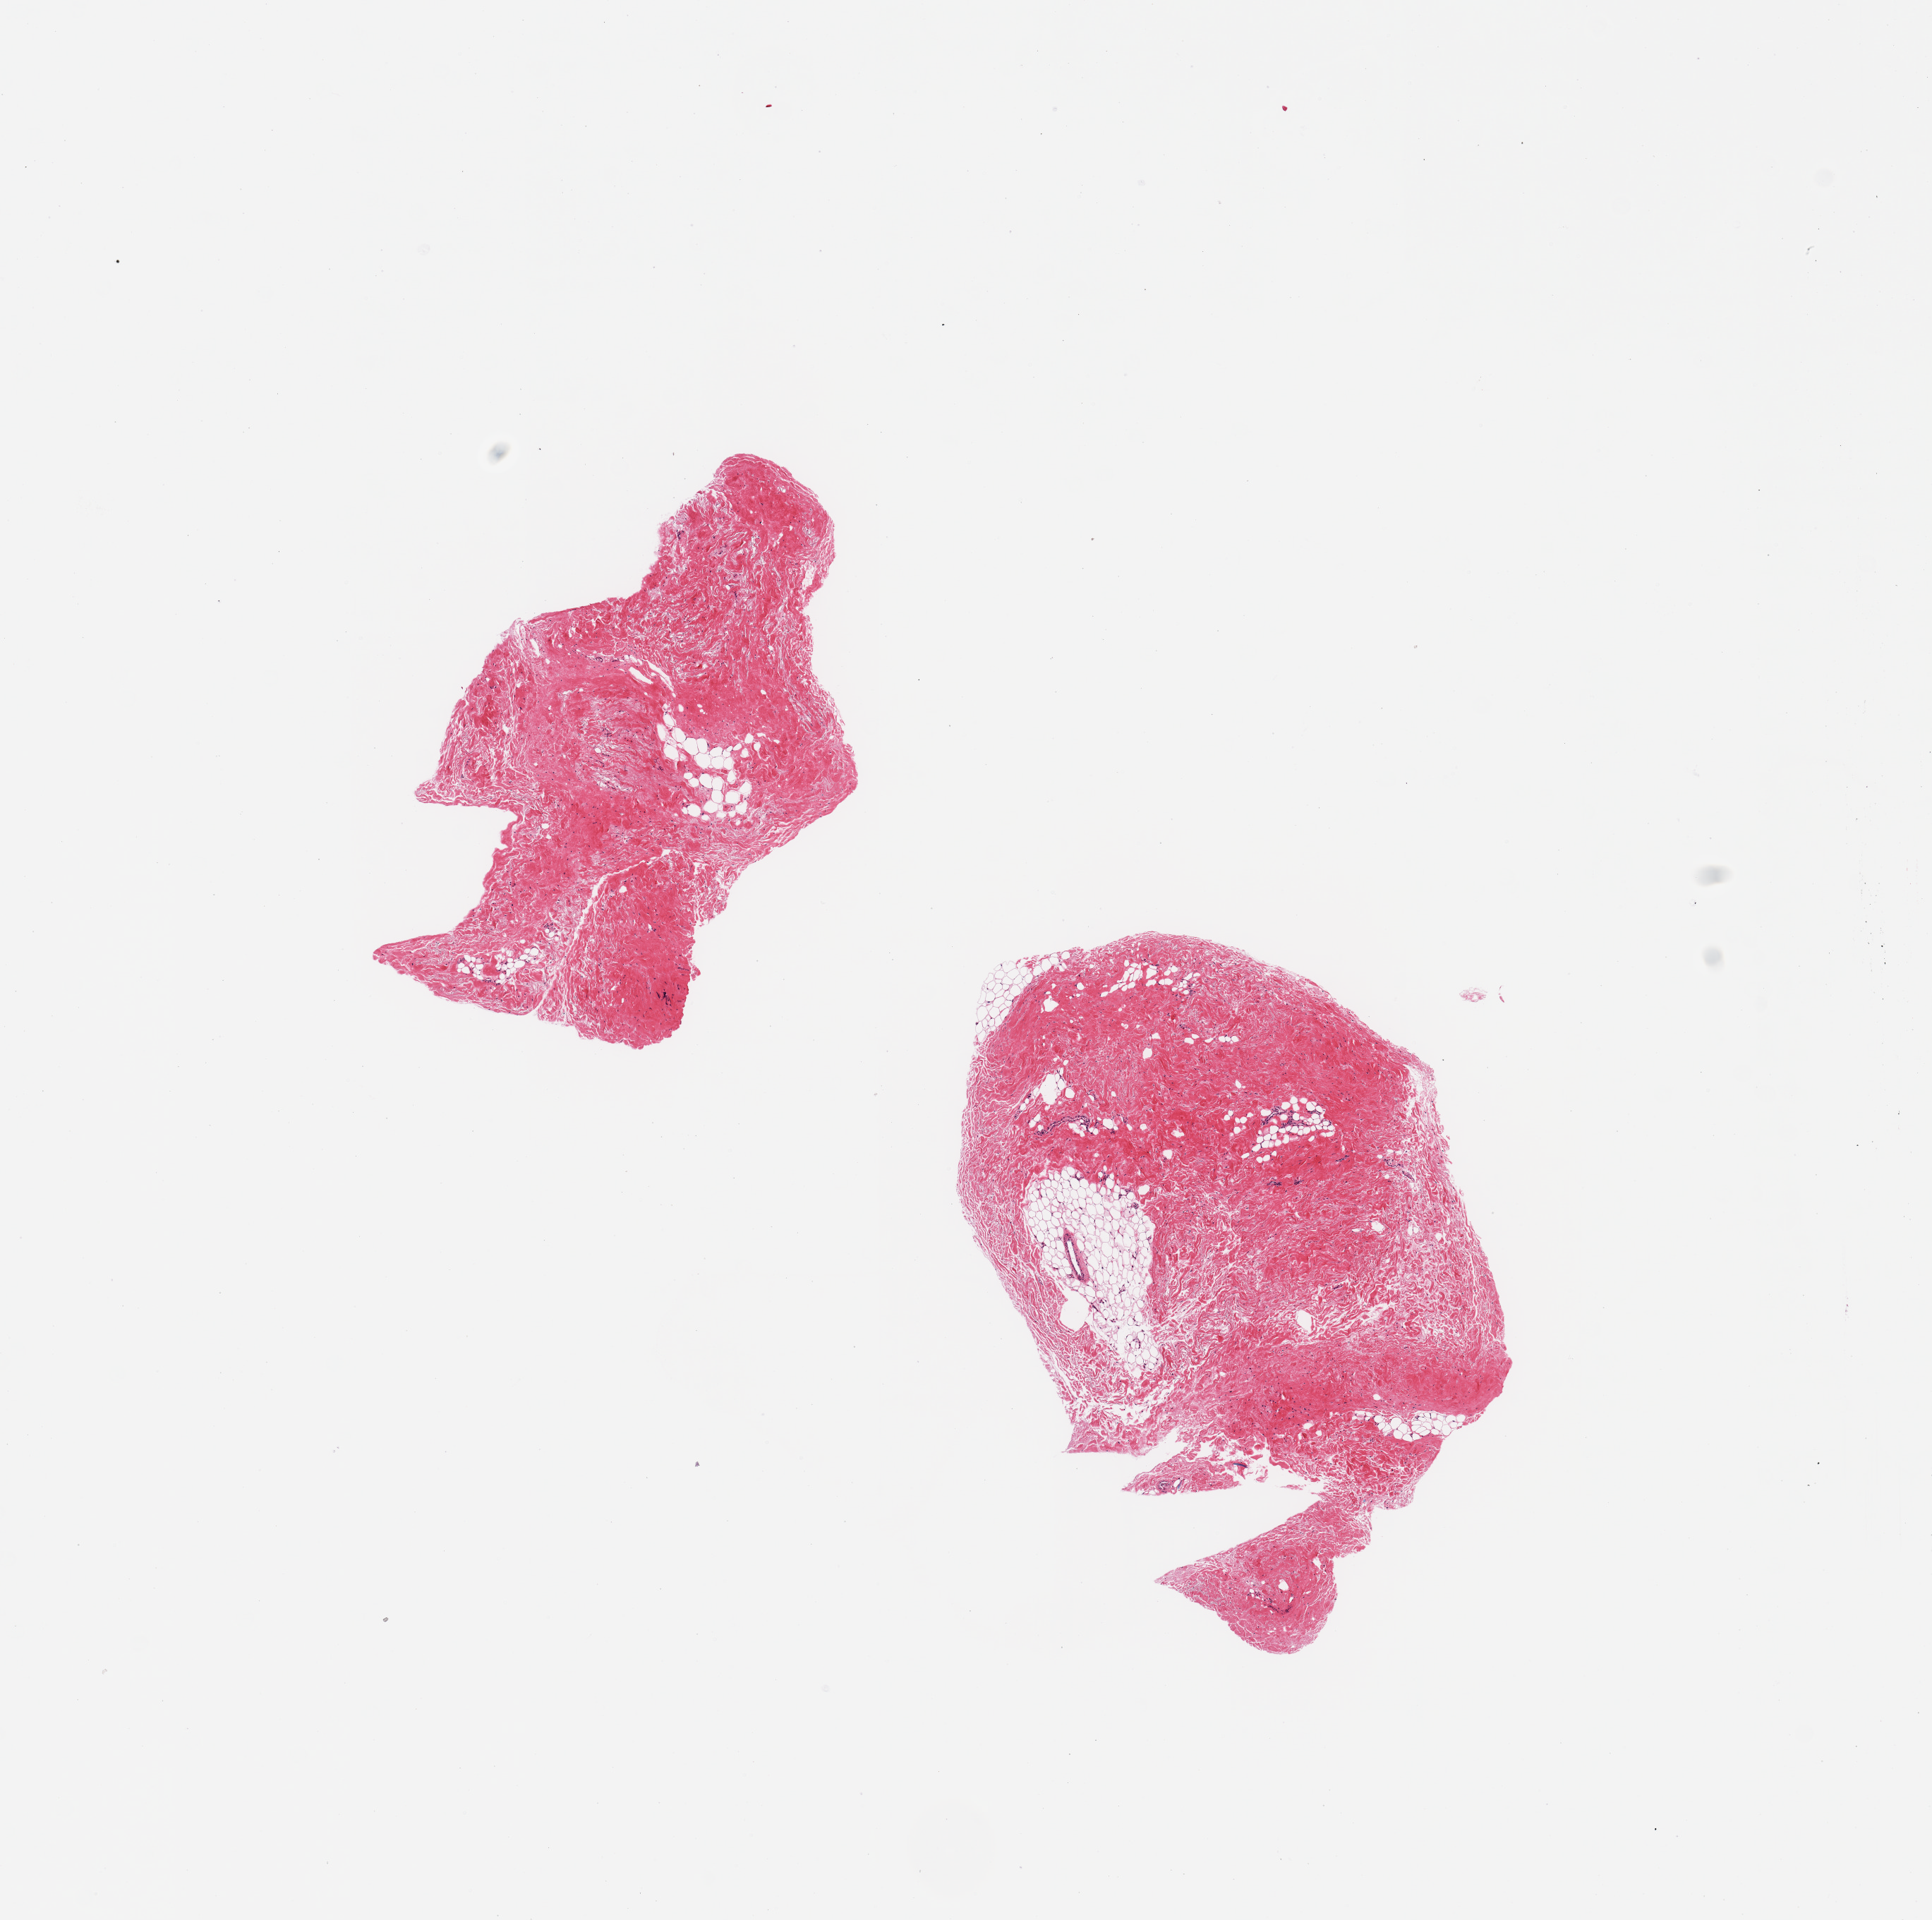
Digitized hematoxylin and eosin (H&E)-stained section, brightfield, shown as a low-resolution overview of the whole scanned area (about 10.8 x 10.8 mm, acquisition: 20x scan). PAXgene-fixed, paraffin-embedded tissue. Target tissue: breast. Tissue donor sample. Donor: male.
- pathologist's review note for this sample: 2 pieces, gynecomatoid stromal hyperplasia